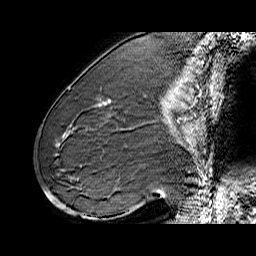
Breast MRI (dynamic contrast-enhanced), one sagittal slice; slice 27 of 60 in the series (ordered by position); dynamic contrast-enhanced series, time point 2 of 6 at this slice position (early post-contrast); 1.5 T; TE 6.4 ms, TR 32.9 ms; 256 × 256 image matrix, field of view 200 × 200 mm. Female patient. Case-level facts recorded for this patient, not image findings: setting: breast cancer imaged before/during neoadjuvant chemotherapy; receptor status: HER2-positive.
Outlined on this slice (semi-automatic segmentation, software-assisted and operator-edited):
- analysis volume of interest (the breast-tissue region the enhancement analysis was run in; not a lesion): bounding box [x1, y1, x2, y2] px = [71, 80, 155, 146]
- tumour enhancement mask (voxels above the 100 % enhancement threshold inside the analysis volume of interest): [101, 100, 110, 104]